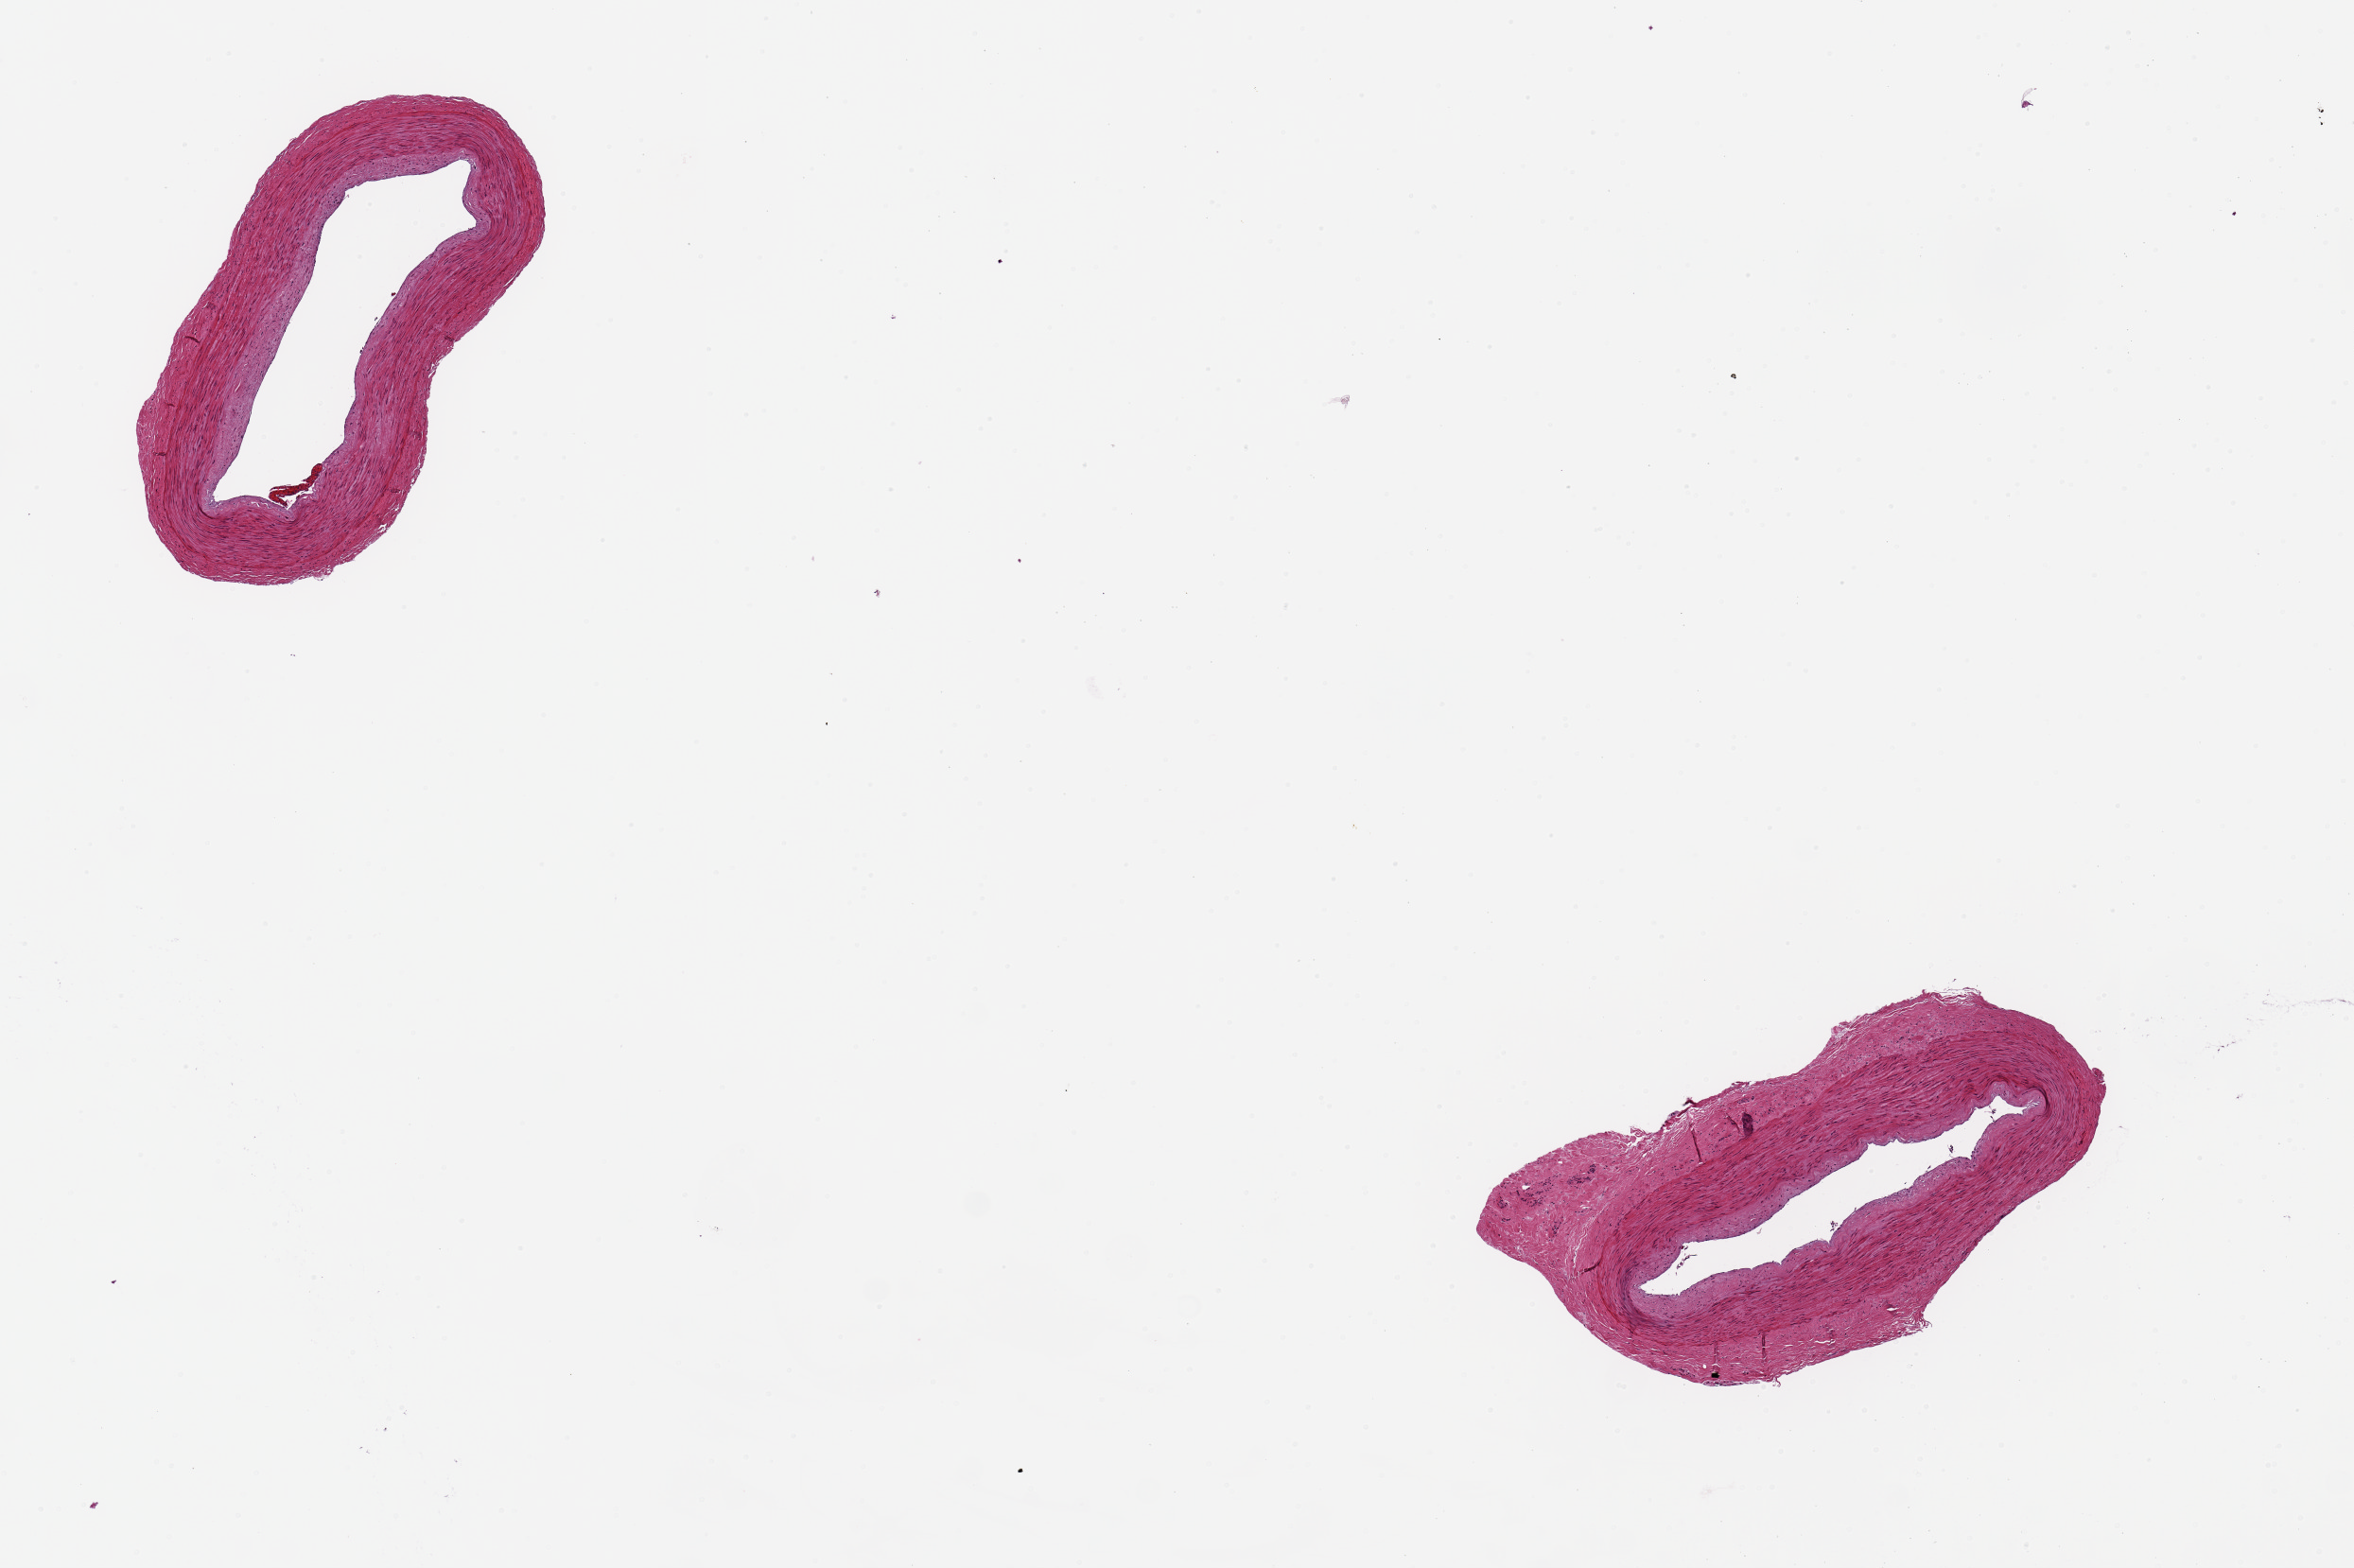
H&E whole-slide image, brightfield, a low-resolution overview of the entire scanned area, about 9.8 x 6.6 mm (slide scanned at 20x). PAXgene-fixed paraffin-embedded (PFPE) section. Sampled site (target tissue): tibial artery. Donor tissue sample. Donor: female.
Reviewer comment on this tissue sample: 2 pieces. 2x1 & 3x1mm; well dissected, adipose free; no lesions.